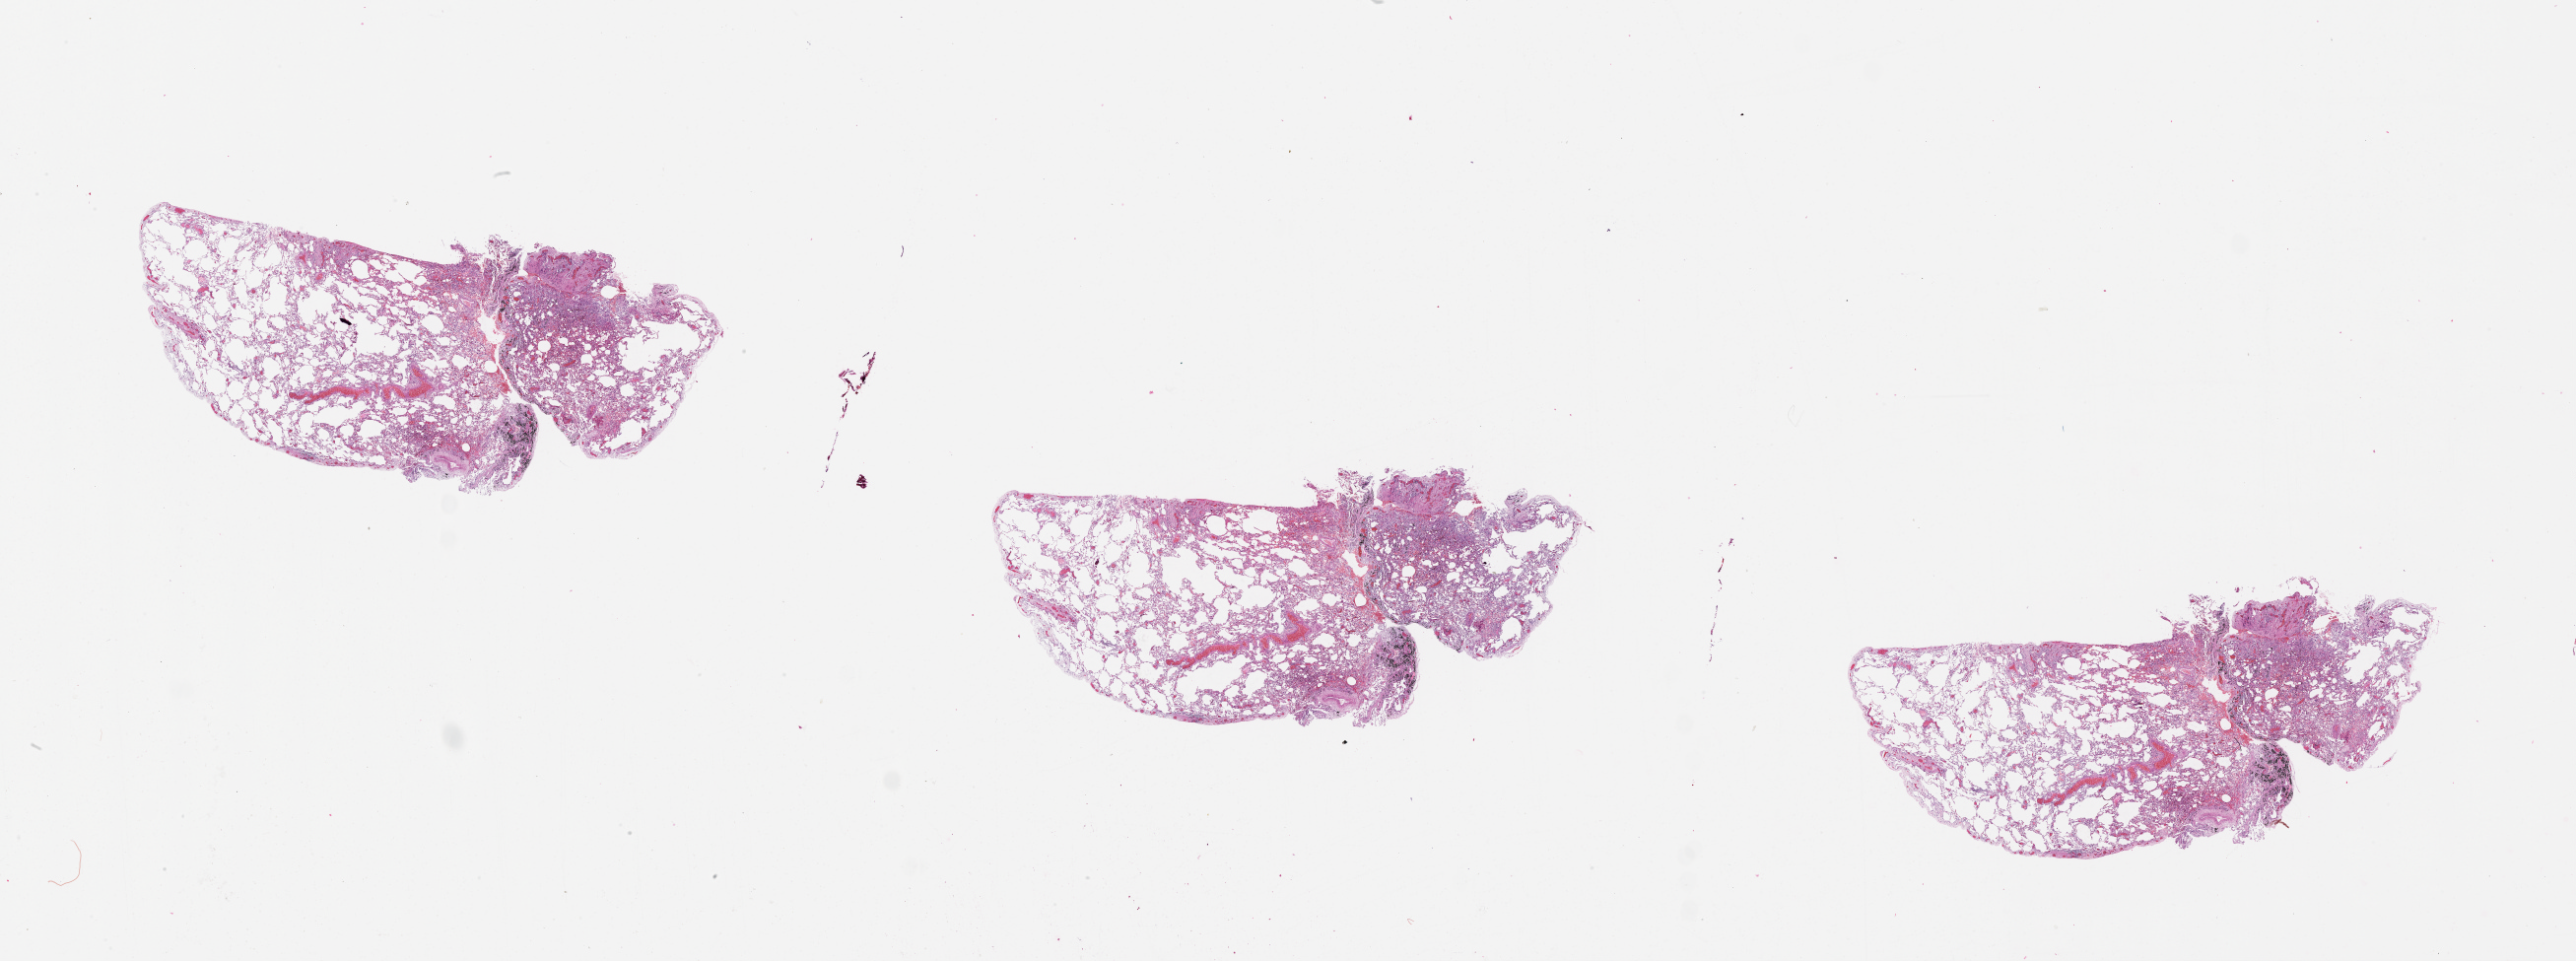
H&E whole-slide image, a low-resolution overview of the entire scanned area, about 42.1 x 15.7 mm, lung, tissue type not recorded.
* patient diagnosis (cohort enrolment): lung adenocarcinoma (lung)